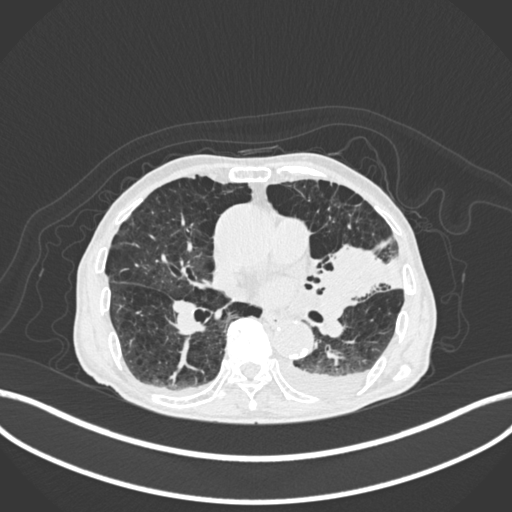
Chest CT, one axial slice. Slice 107 of 400 in the series (ordered by position). 120 kVp. Lung window (W 1500 / L -600 HU). 512 × 512 image matrix, field of view 400 × 400 mm. Male patient, age 90 years or older. Case-level facts recorded for this patient, not image findings: clinical TNM (as recorded): T2b N1 M0.
Structures marked on this image (rectangle marked by the reading radiologist):
- lung tumour (recorded histology: squamous cell carcinoma): bounding box [x1, y1, x2, y2] px = [321, 243, 387, 300]